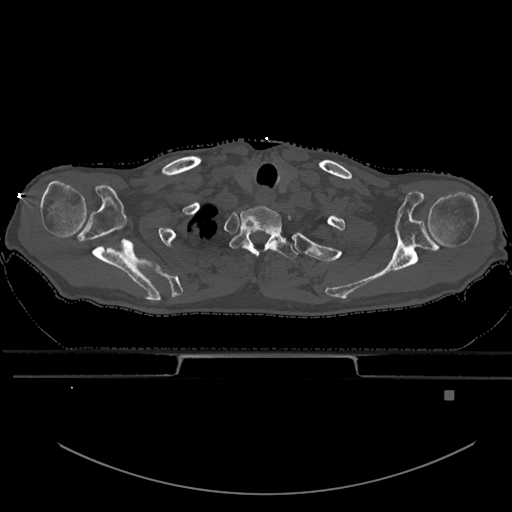
CT including the spine, one axial slice. Position 546 of 969 along the scan axis. Bone window (W 1800 / L 400 HU). 0.5 mm slice thickness. 512 × 512 image matrix. Patient: male, 82 years. Case-level facts recorded for this patient, not image findings: primary cancer: prostate.
Structures marked on this image (semi-automatically segmented with operator editing):
- T1 vertebra: bounding box <230,226,298,259> (left, top, right, bottom; pixels)